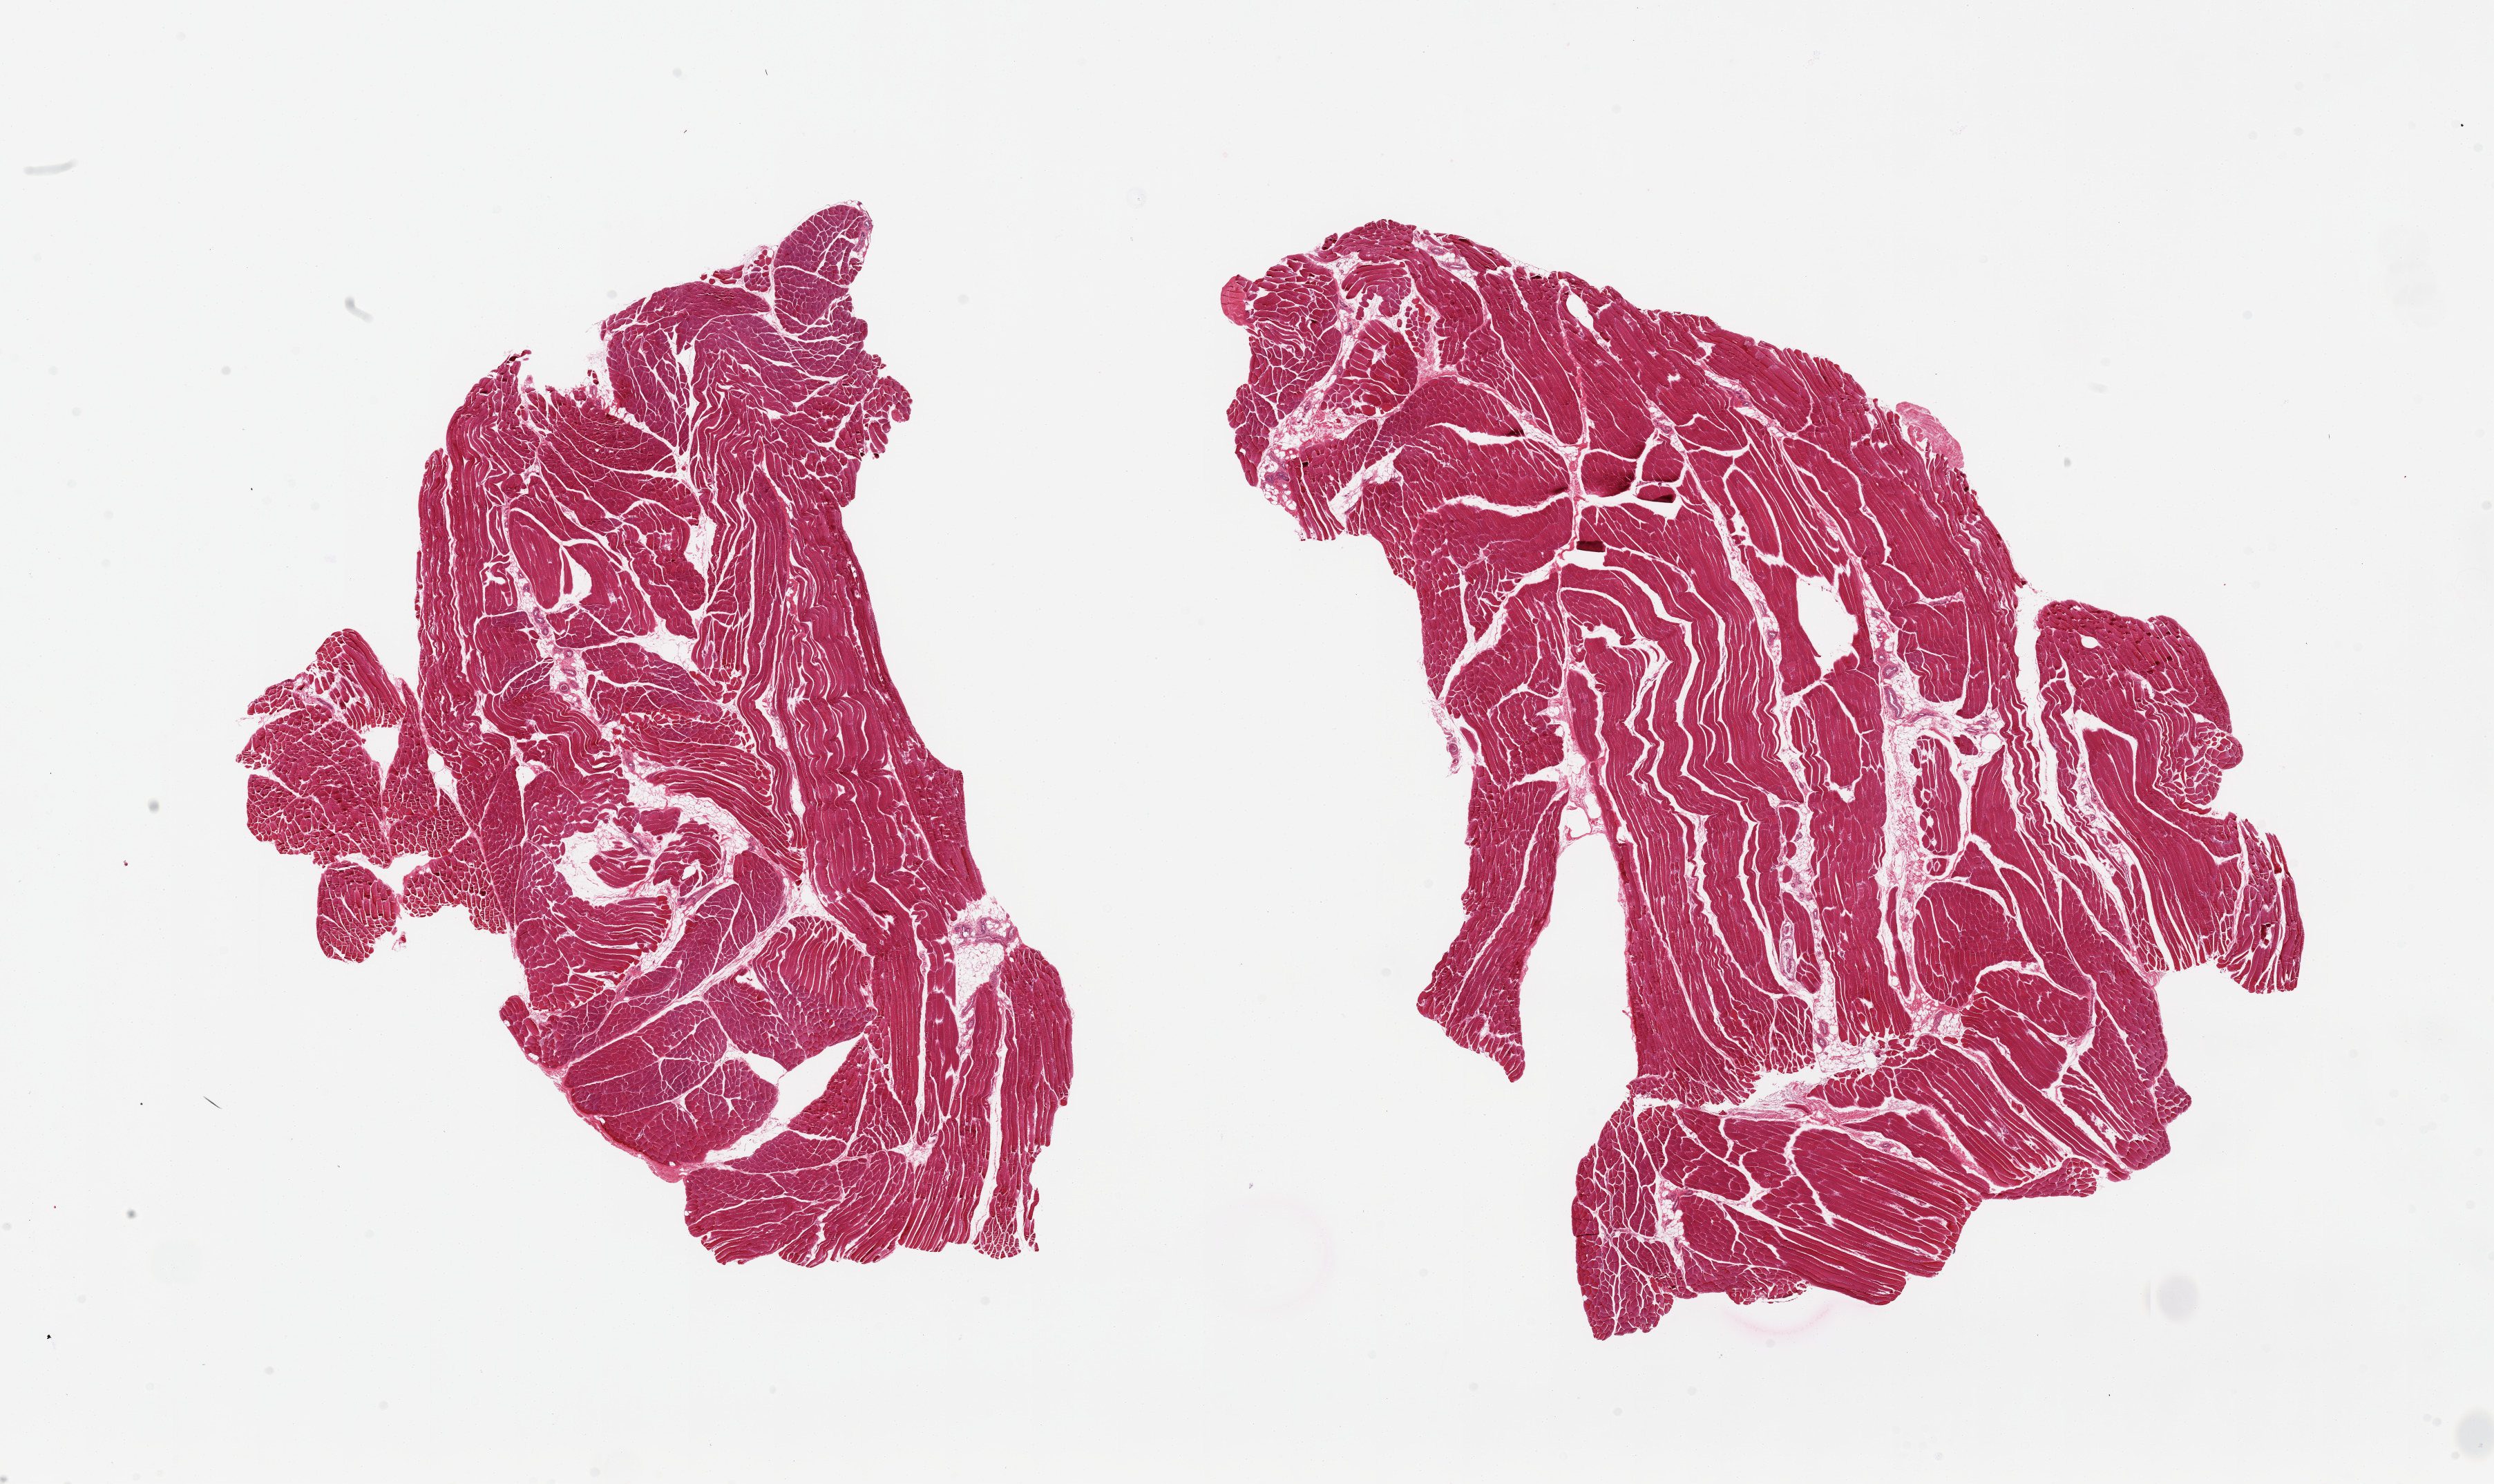
Digitized hematoxylin and eosin (H&E)-stained section, whole scanned area (about 28.5 x 17.0 mm) shown as a low-resolution overview. PAXgene-fixed paraffin-embedded (PFPE) section. Target tissue: skeletal muscle. Donor tissue sample.
Review note (as recorded): 2 pieces, 12x8.5 and 14x9mm; well trimmed. <5% internal fat.